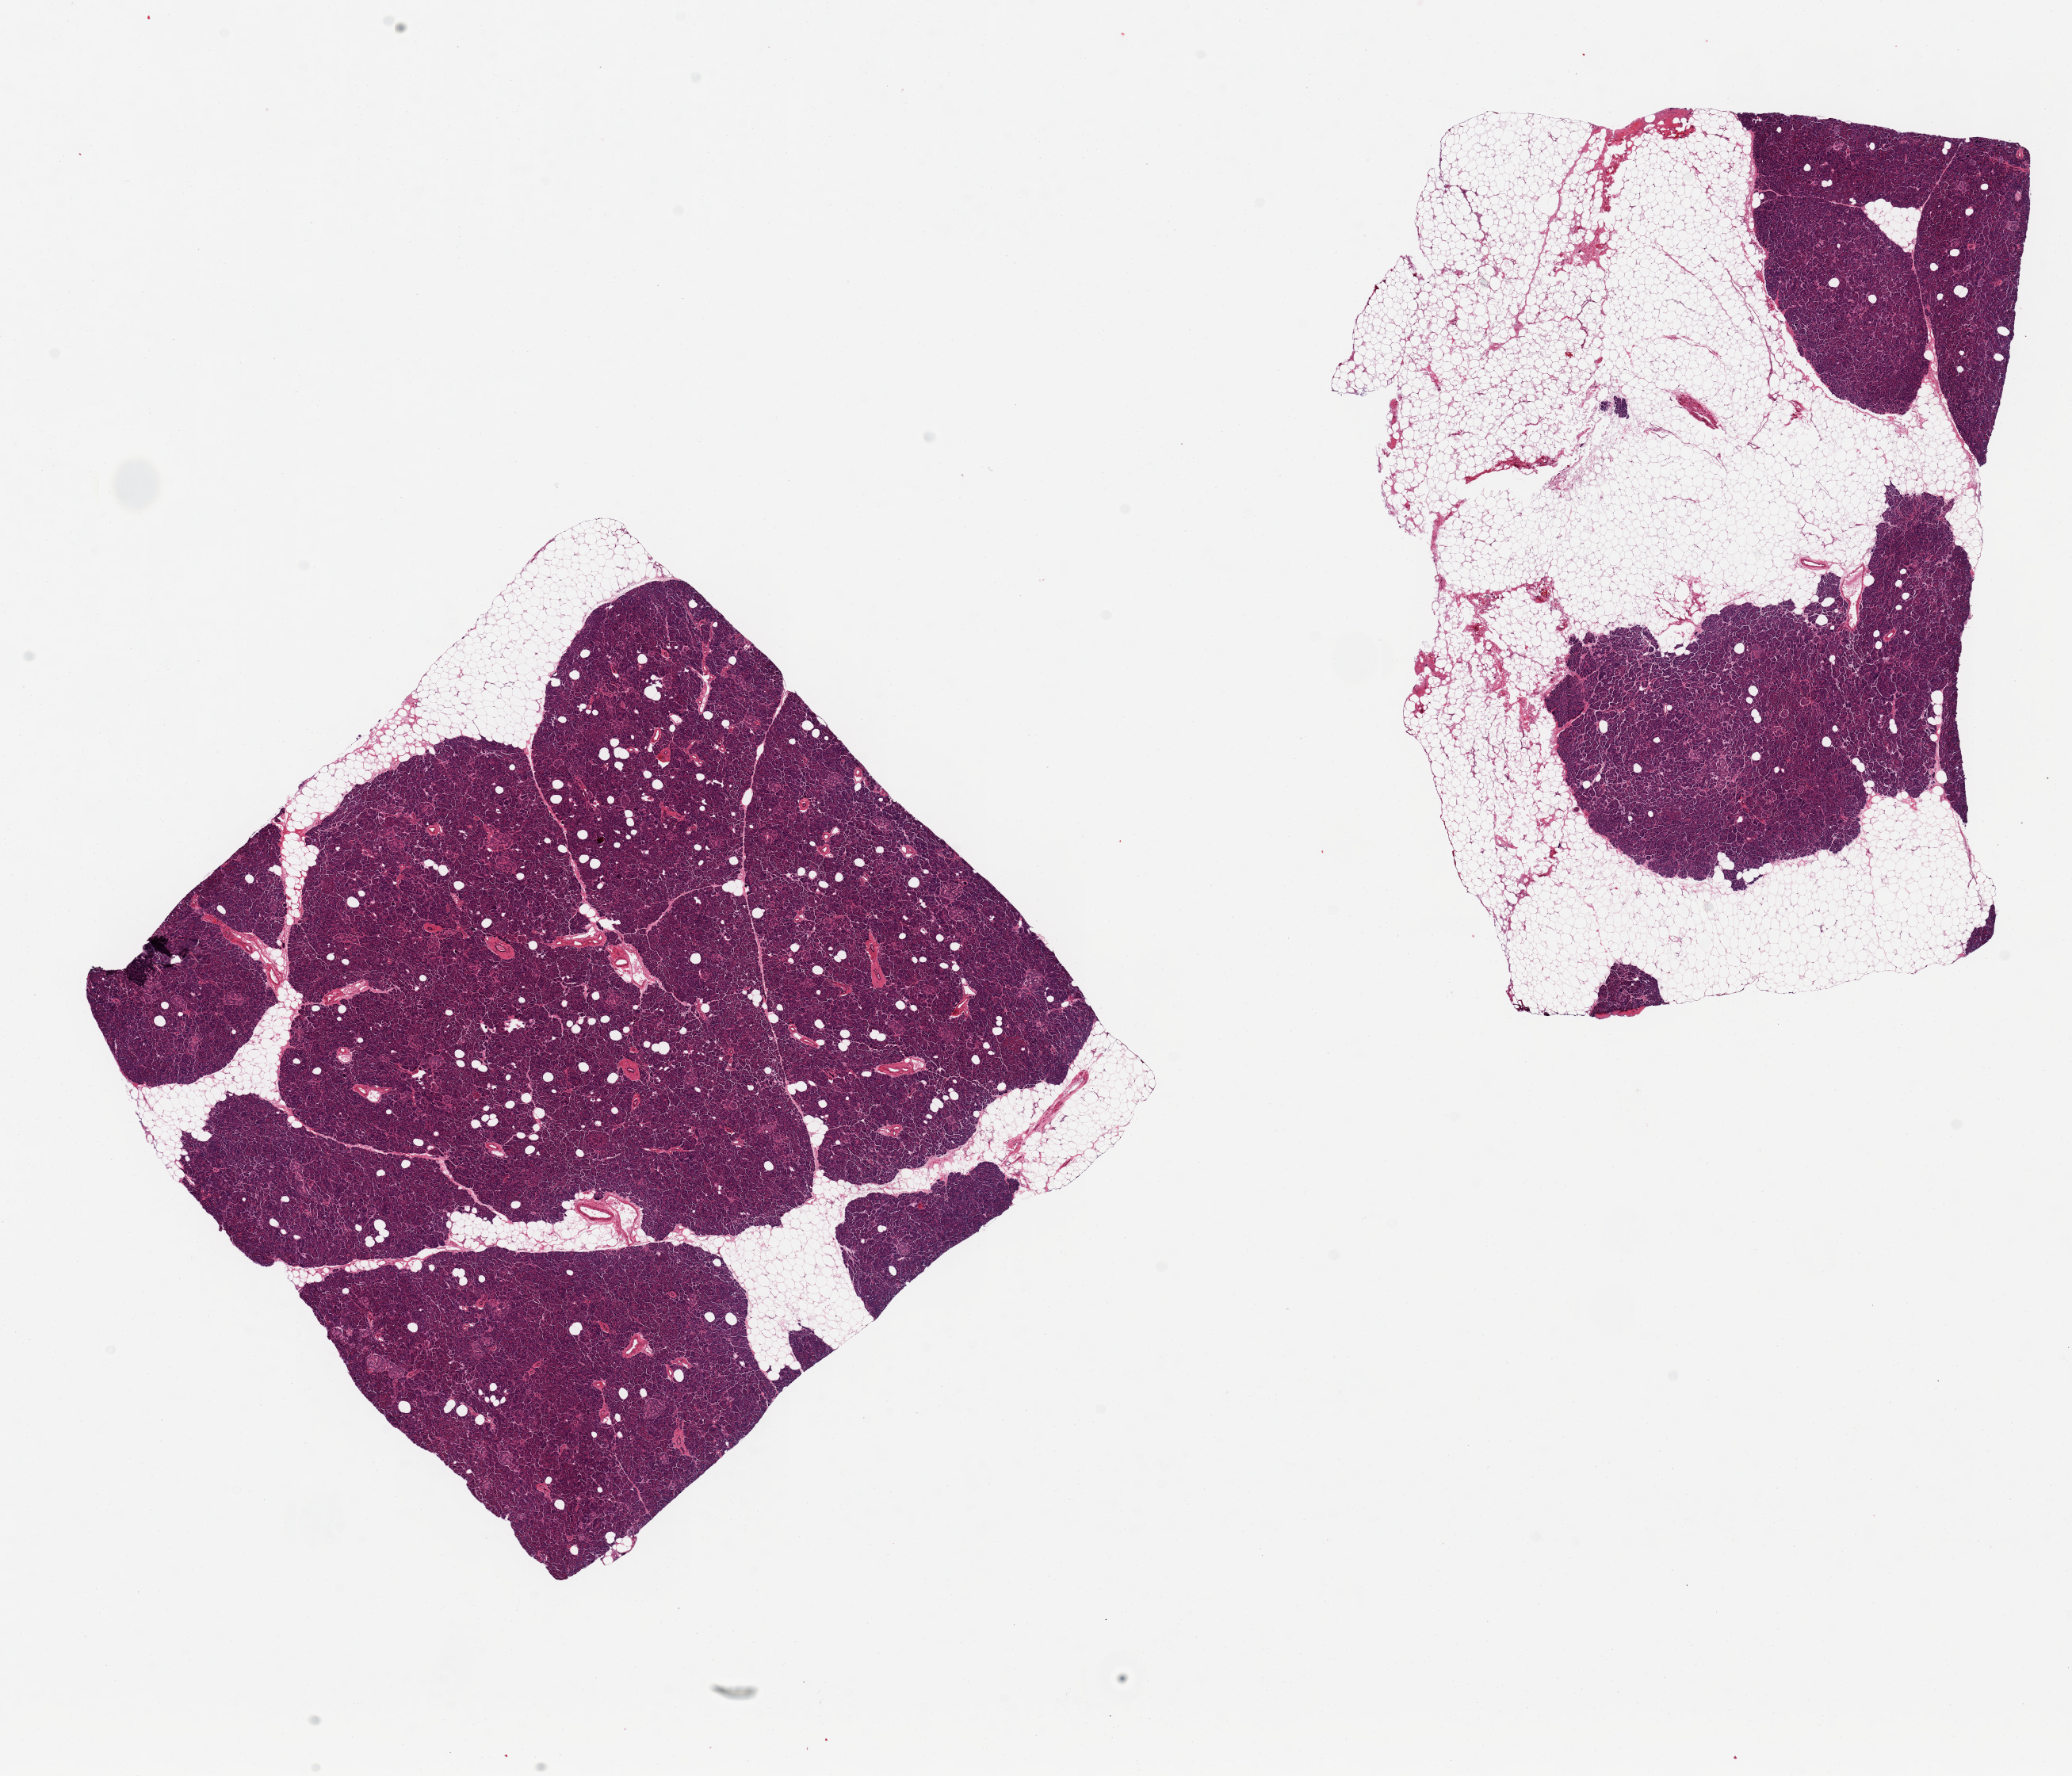
Whole-slide image, H&E stain, brightfield — whole scanned area (about 20.7 x 17.7 mm) shown as a low-resolution overview. PAXgene-fixed, paraffin-embedded tissue. Section of pancreas (target tissue). Tissue donor sample. Male donor.
- reviewer comment on this tissue sample: 2 pieces 7.9x7.7 & 9x5 mm; 1 with 60%, other 10% adipose